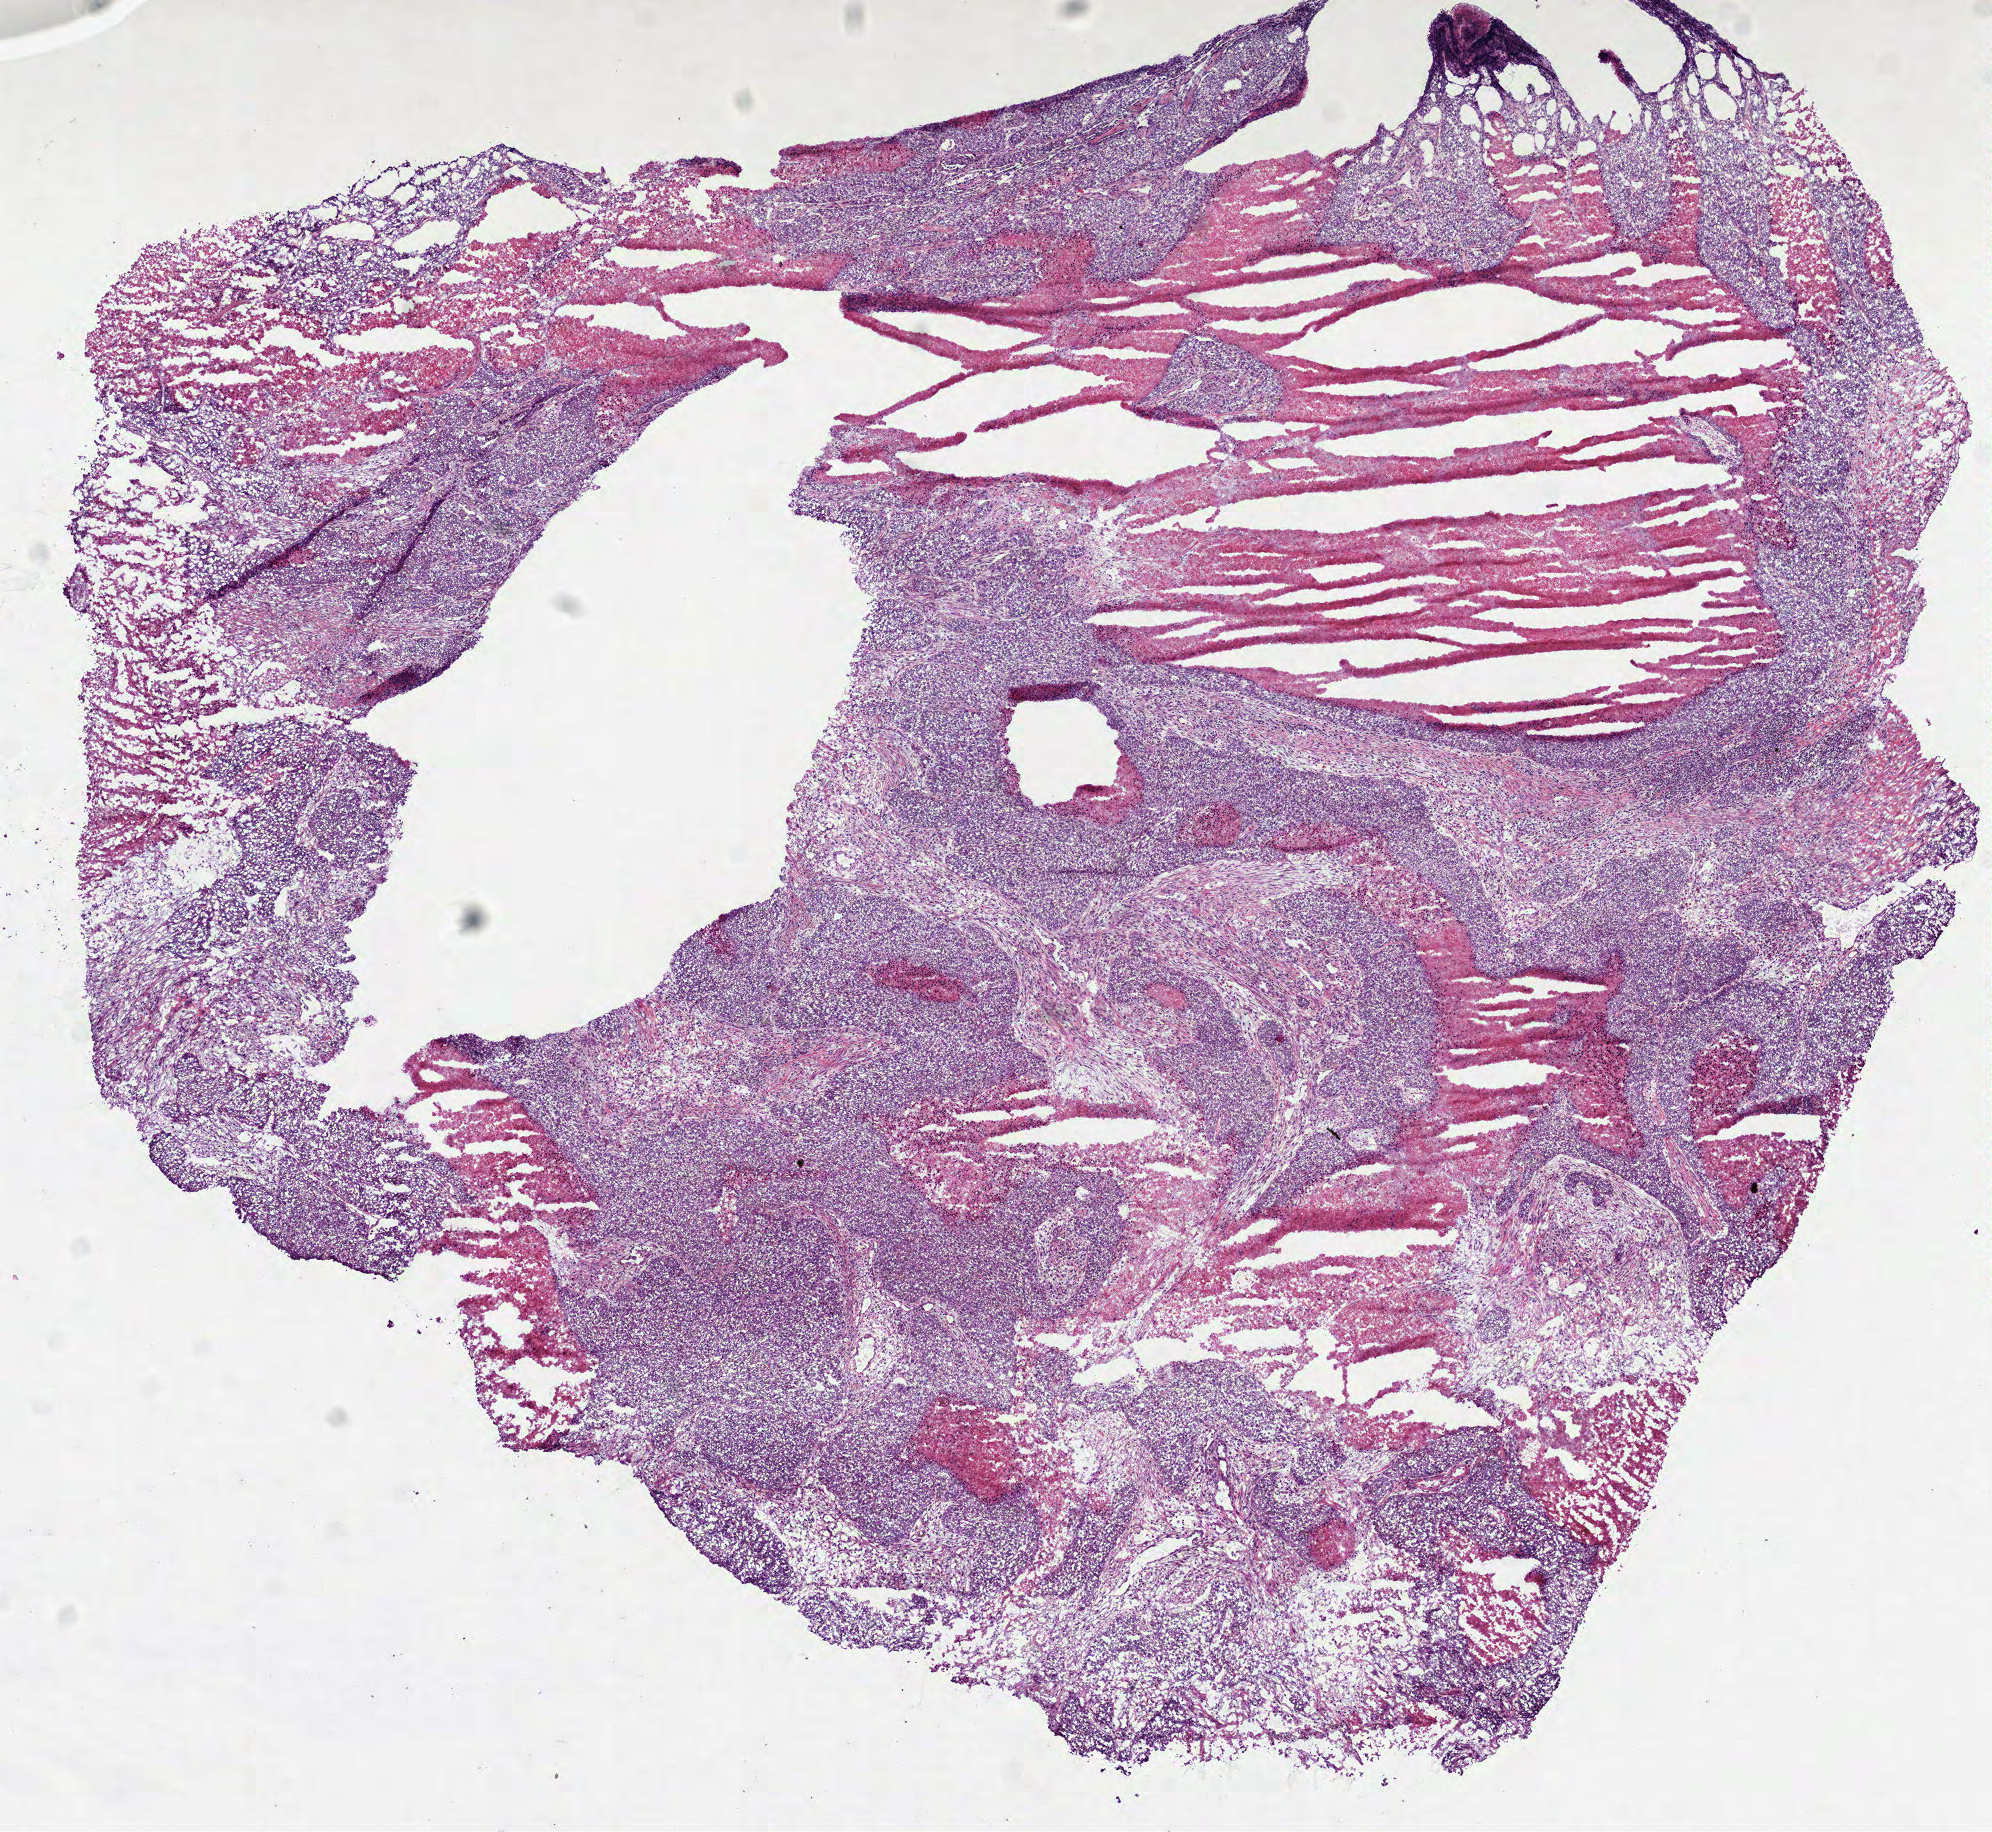
Whole-slide histology image, Hematoxylin and eosin (H&E) stained, shown as a low-resolution overview of the whole scanned area (about 8.0 x 7.4 mm). Frozen section from the bottom of the tissue portion. Lung, primary tumour sample. Female, age 78 years at initial diagnosis. Pathologist review of this section (percent, as recorded): tumour cells 61%, tumour nuclei 80%, normal cells 0%, stromal cells 0%, necrosis 39%. Infiltration values recorded for this section: lymphocyte infiltration 10%, monocyte infiltration 0%, neutrophil infiltration 2%.
• pathologic diagnosis: Squamous cell carcinoma, NOS (upper lobe, lung)
• AJCC pathologic stage: IB